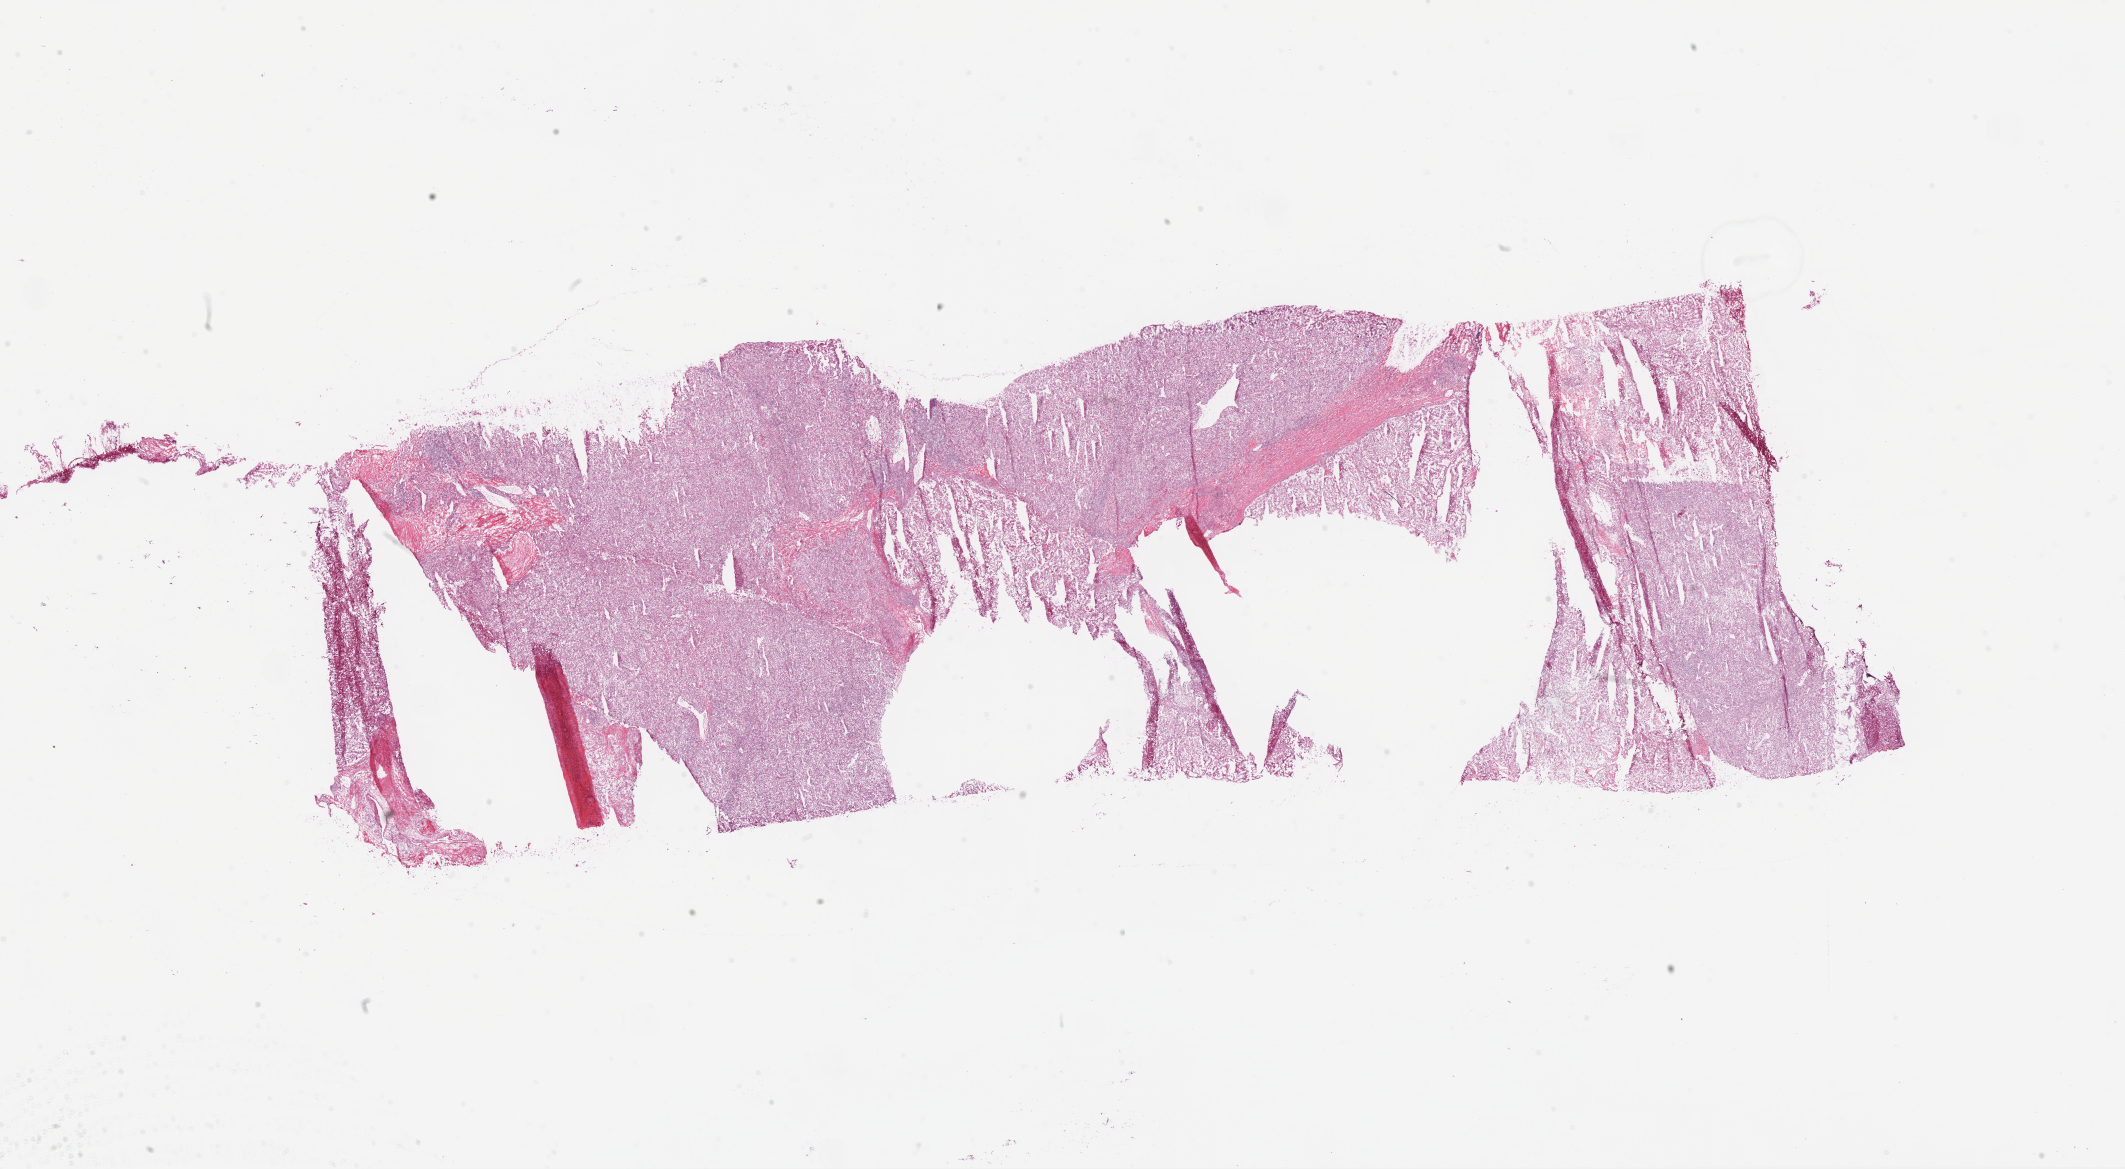
Whole-slide histology image, Hematoxylin and eosin (H&E) stained — whole scanned area (about 34.1 x 18.8 mm) shown as a low-resolution overview. Frozen section from the bottom of the tissue portion. Primary tumour sample from the kidney. Female, age 55 years at initial diagnosis. Histologic grade: G4 (undifferentiated). Composition of this section per pathologist review: tumour cells 90%, tumour nuclei 75%, normal cells 0%, stromal cells 10%, necrosis 0%.
Histologic diagnosis: Clear cell adenocarcinoma, NOS. AJCC pathologic stage: IV.